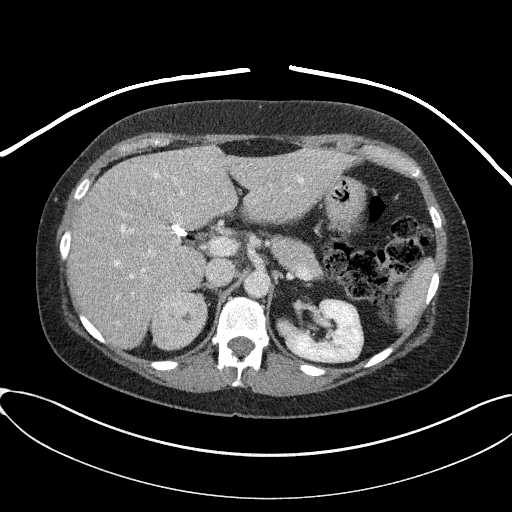
Contrast-enhanced abdominal CT, one axial slice. Position 54 of 95 along the scan axis. Reconstruction kernel I41f/2. Intravenous contrast given. Soft-tissue window (W 400 / L 40 HU). 512 × 512 image matrix, field of view 410 × 410 mm. Patient: female, 46 years. From the clinical record (not read from this slice): diagnosis: adrenocortical carcinoma; tumour side: right adrenal; tumour size at pathology: 7.2 cm.
Annotated regions visible in this slice (semi-automatic segmentation, software-assisted and operator-edited):
- mass: bounding box [x1, y1, x2, y2] px = [153, 292, 206, 349]